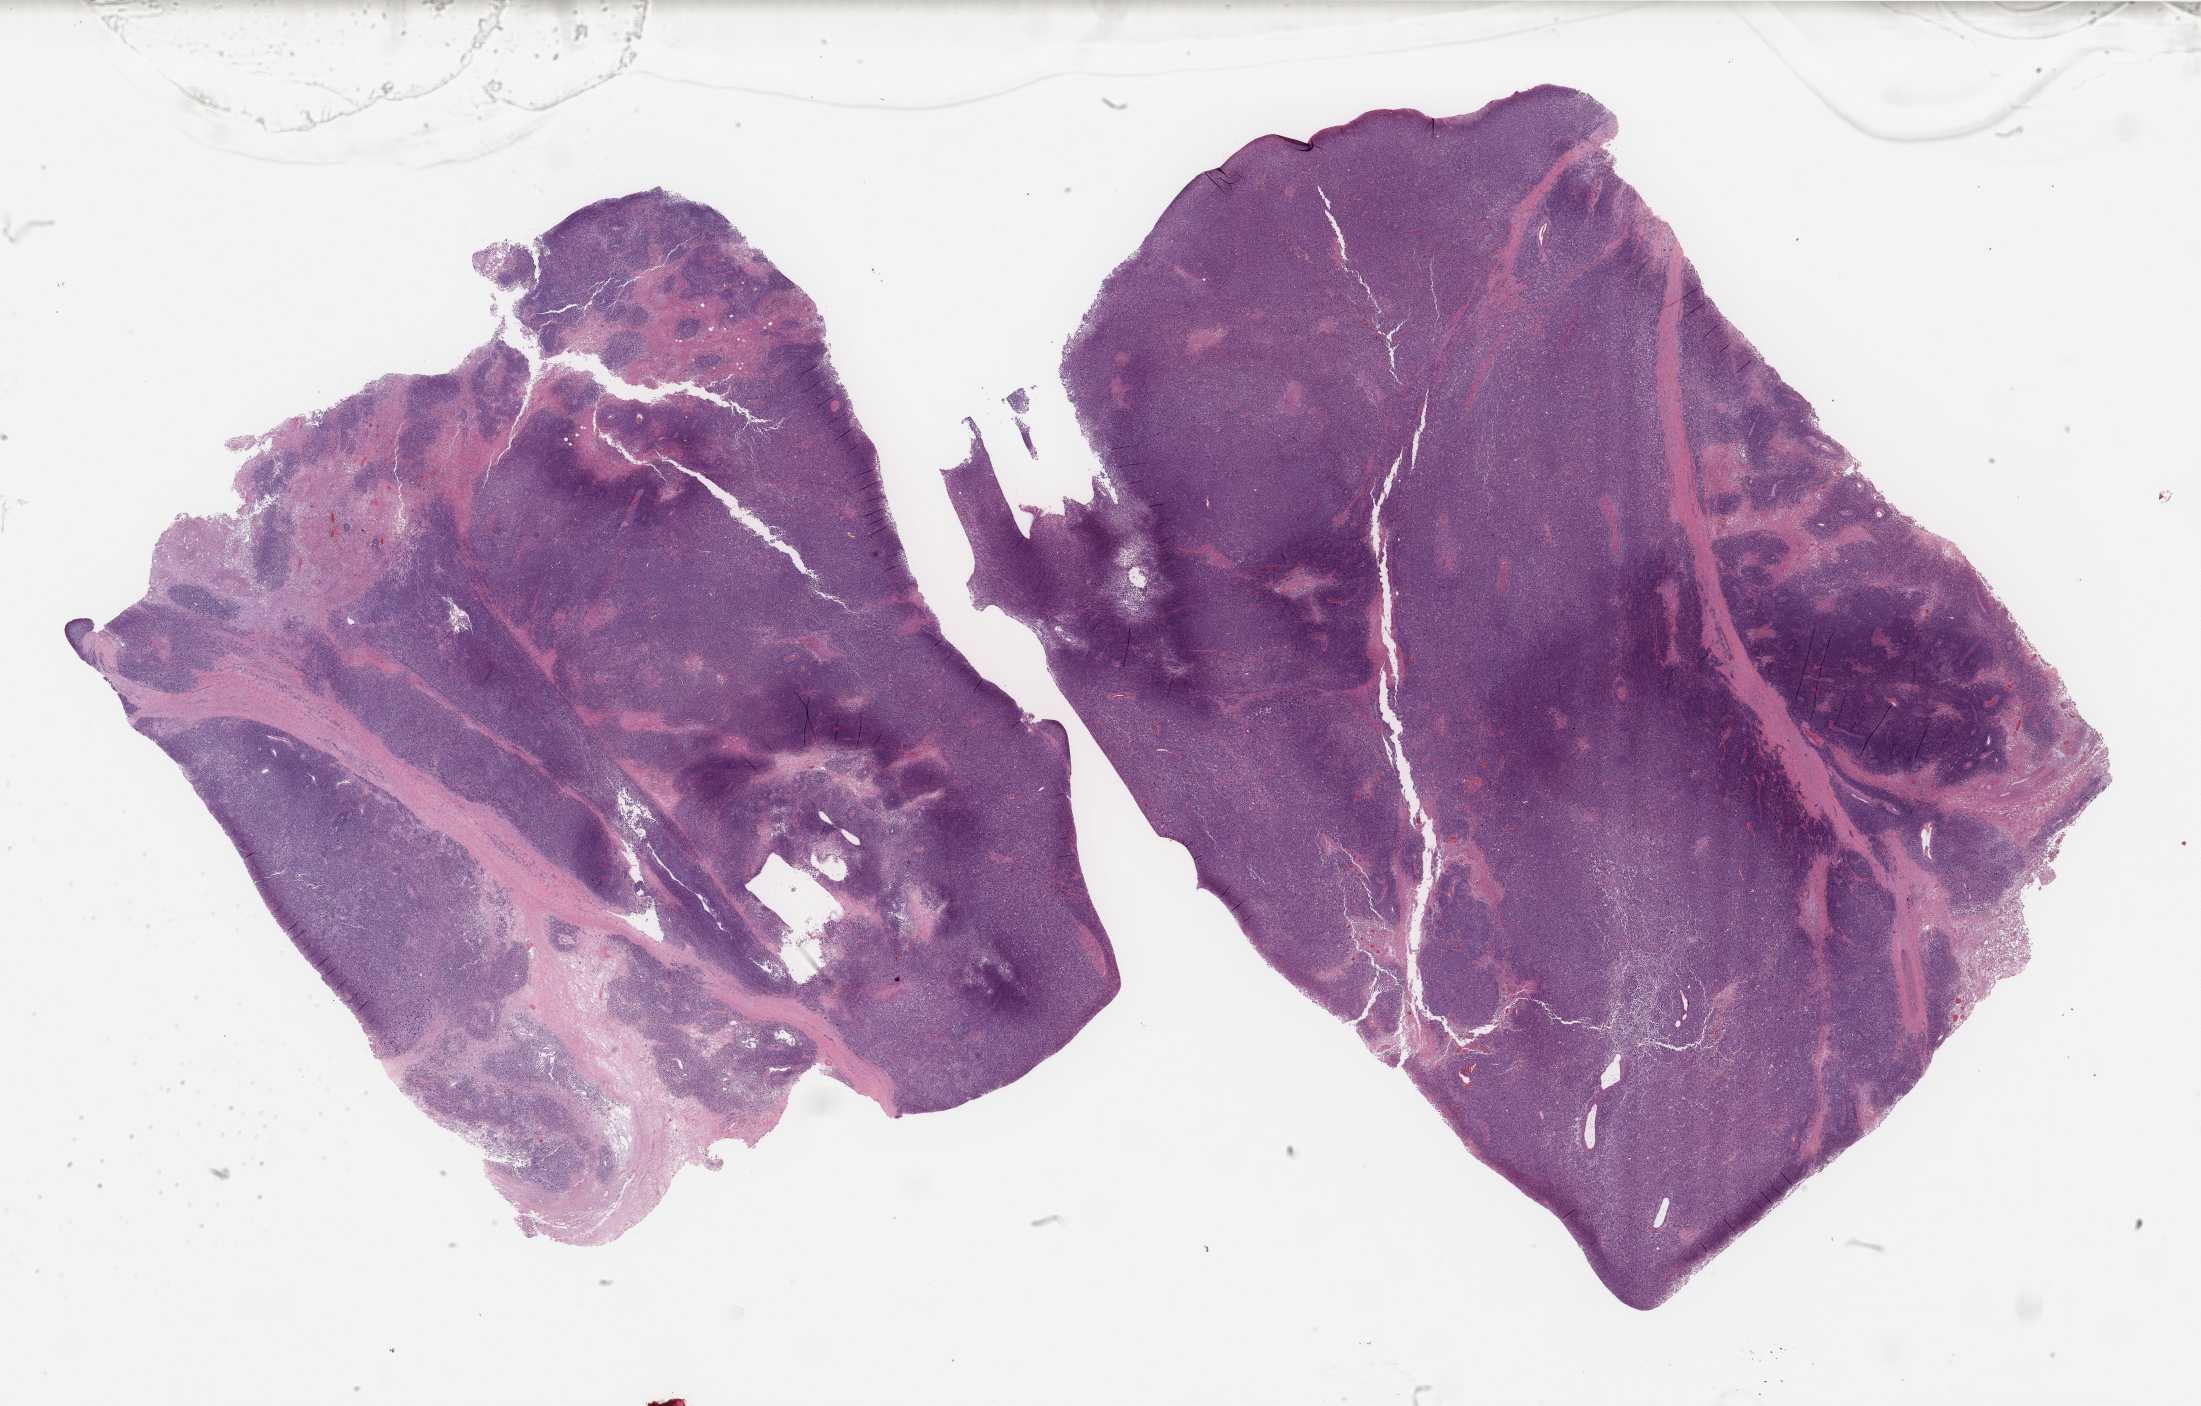
Digitized Hematoxylin and eosin (H&E) stained tissue section (whole slide) — low-resolution overview of the scanned area, about 34.9 x 22.3 mm (acquisition: 40x scan); formalin-fixed paraffin-embedded (FFPE) diagnostic section; skin, primary tumour sample. Male, age 51 years at initial diagnosis.
Histologic diagnosis: Acral lentiginous melanoma, malignant.